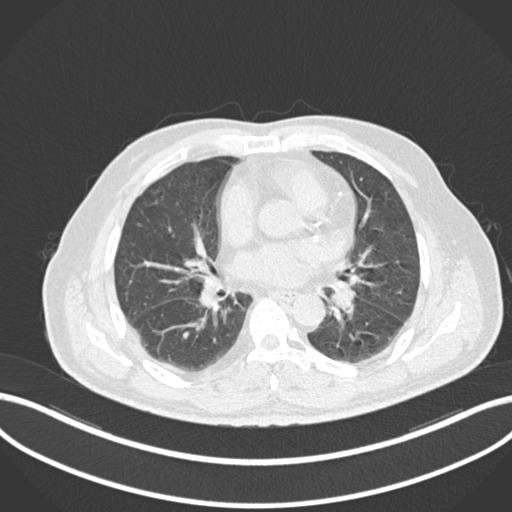
Chest CT, one axial slice; slice 67 of 161 in the series (ordered by position); reconstruction kernel B30f; 120 kVp; lung window (W 1500 / L -600 HU); 1 mm slice thickness; 512 × 512 image matrix, field of view 400 × 400 mm. Patient: male, 71 years. From the clinical record (not read from this slice): clinical TNM (as recorded): T1b N0 M0.
Outlined on this slice (bounding box drawn by a radiologist):
- lung tumour (recorded histology: squamous cell carcinoma): bounding box [x1, y1, x2, y2] px = [330, 284, 357, 314]